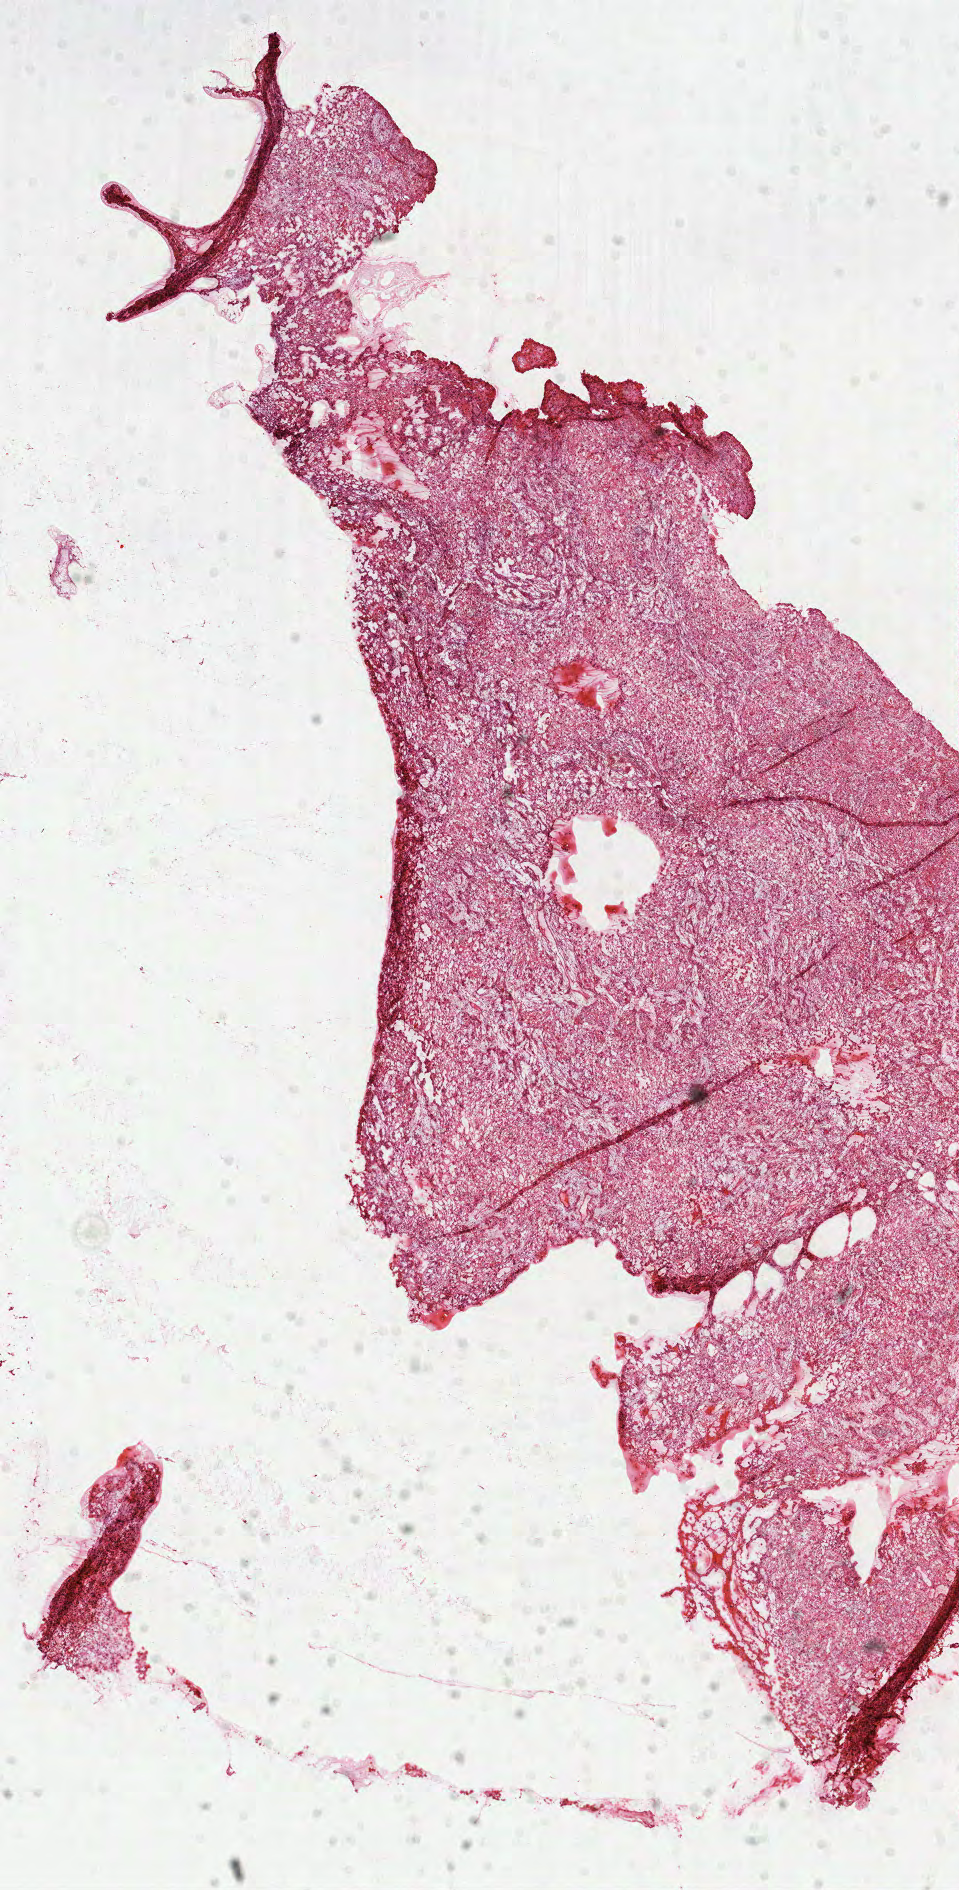
Digitized H&E-stained tissue section (whole slide), low-resolution overview of the scanned area, about 7.7 x 15.2 mm; FFPE section; sample: primary tumour, lung. Male patient; age at initial diagnosis 71 years.
Histologic diagnosis: Squamous cell carcinoma, NOS (upper lobe, lung).